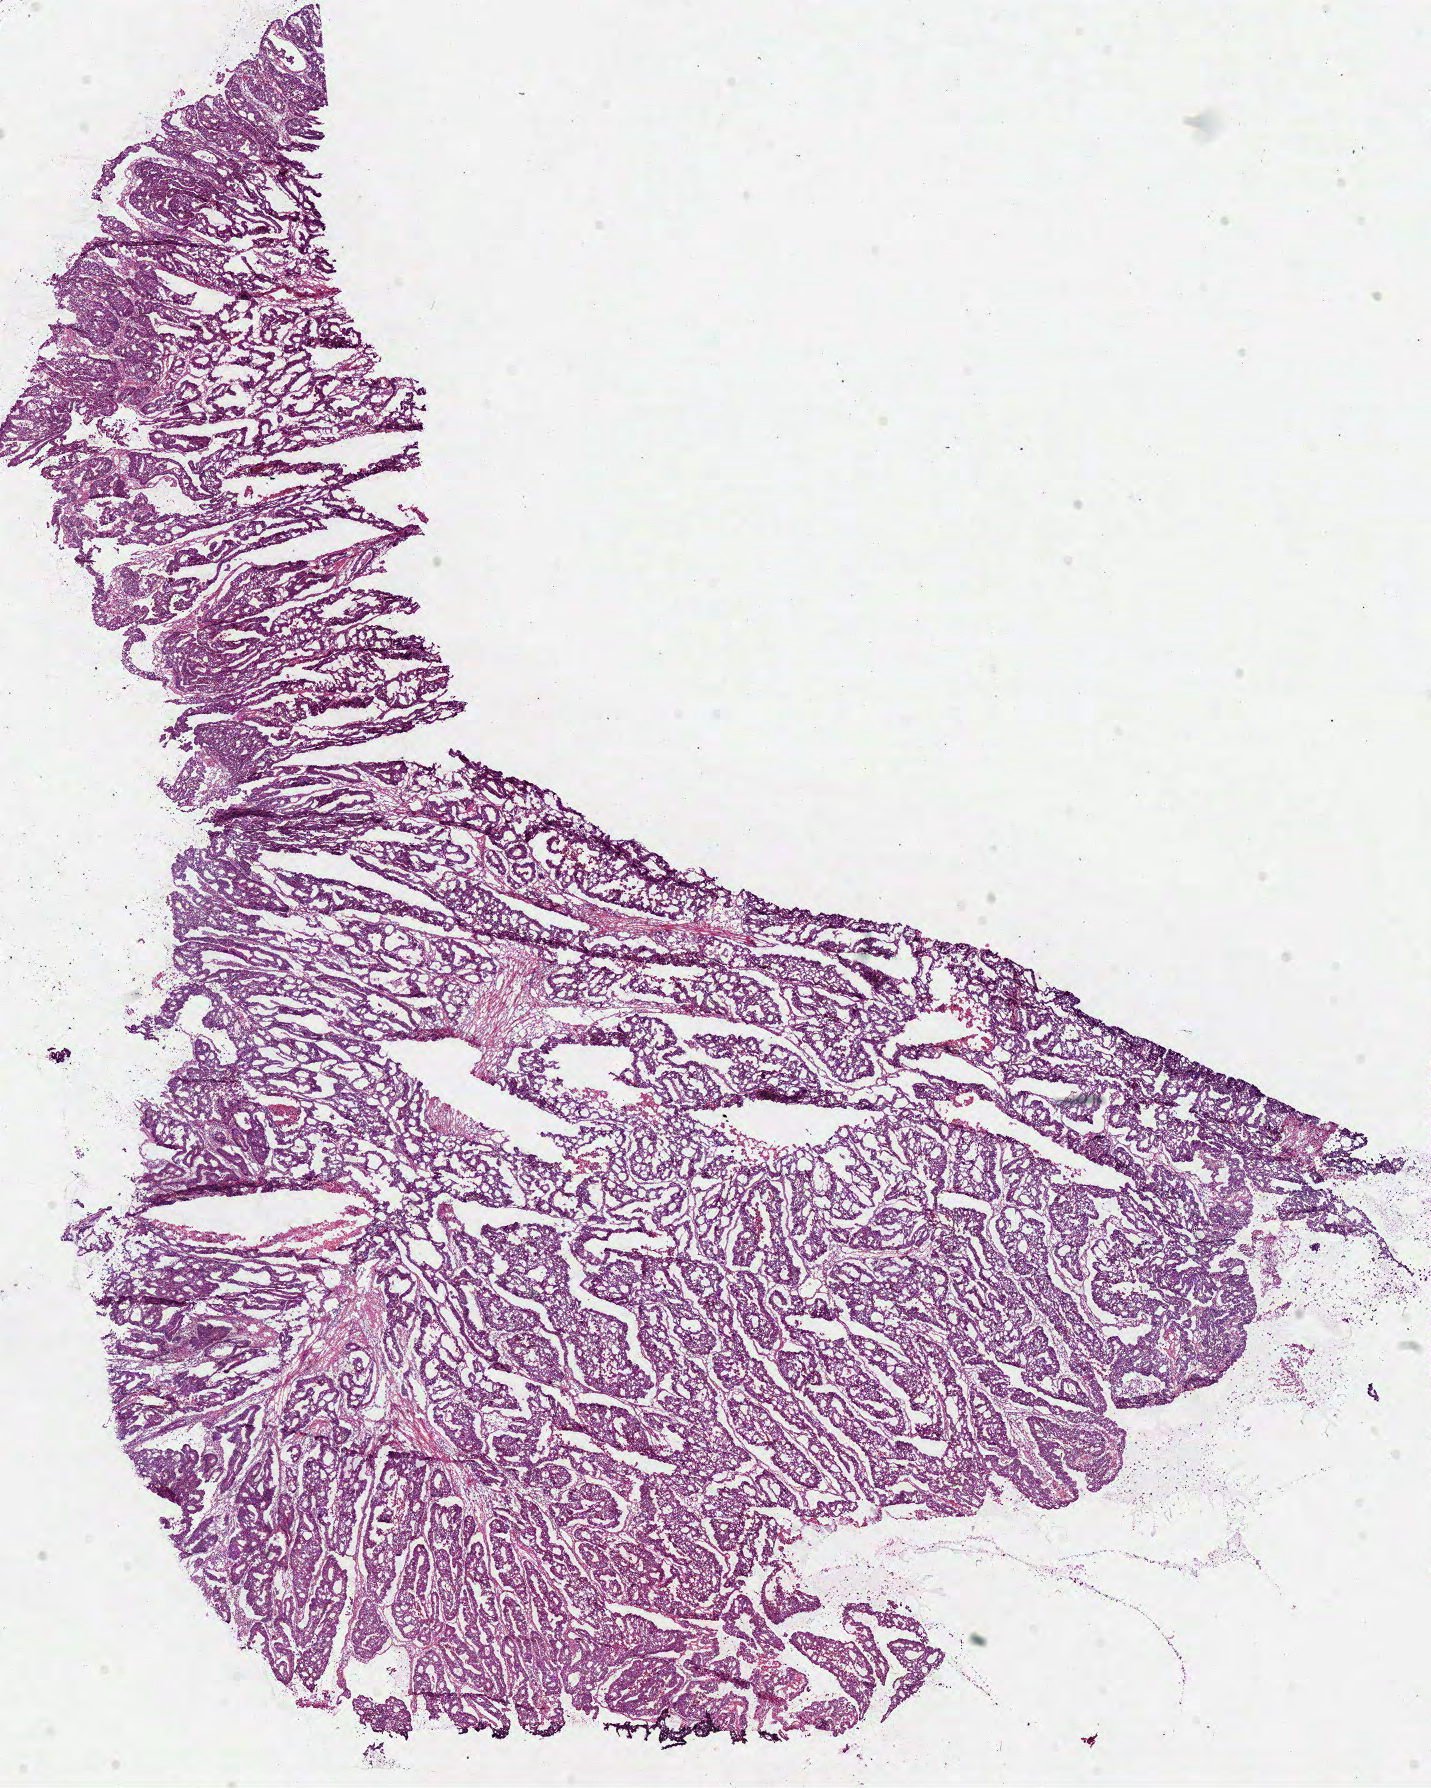
Hematoxylin and eosin (H&E) stained whole-slide image, shown as a low-resolution overview of the whole scanned area (about 11.3 x 14.1 mm, slide scanned at 40x). Frozen section. Primary tumour sample from the colon. Patient: female, age at initial diagnosis 55 years. Composition of this section per pathologist review: tumour cells 87%, tumour nuclei 80%, normal cells 0%, stromal cells 10%, necrosis 3%.
- lymph nodes positive (case pathology): 2 of 12 examined
- pathologic diagnosis: Adenocarcinoma, NOS (sigmoid colon)
- AJCC pathologic stage: IIIA